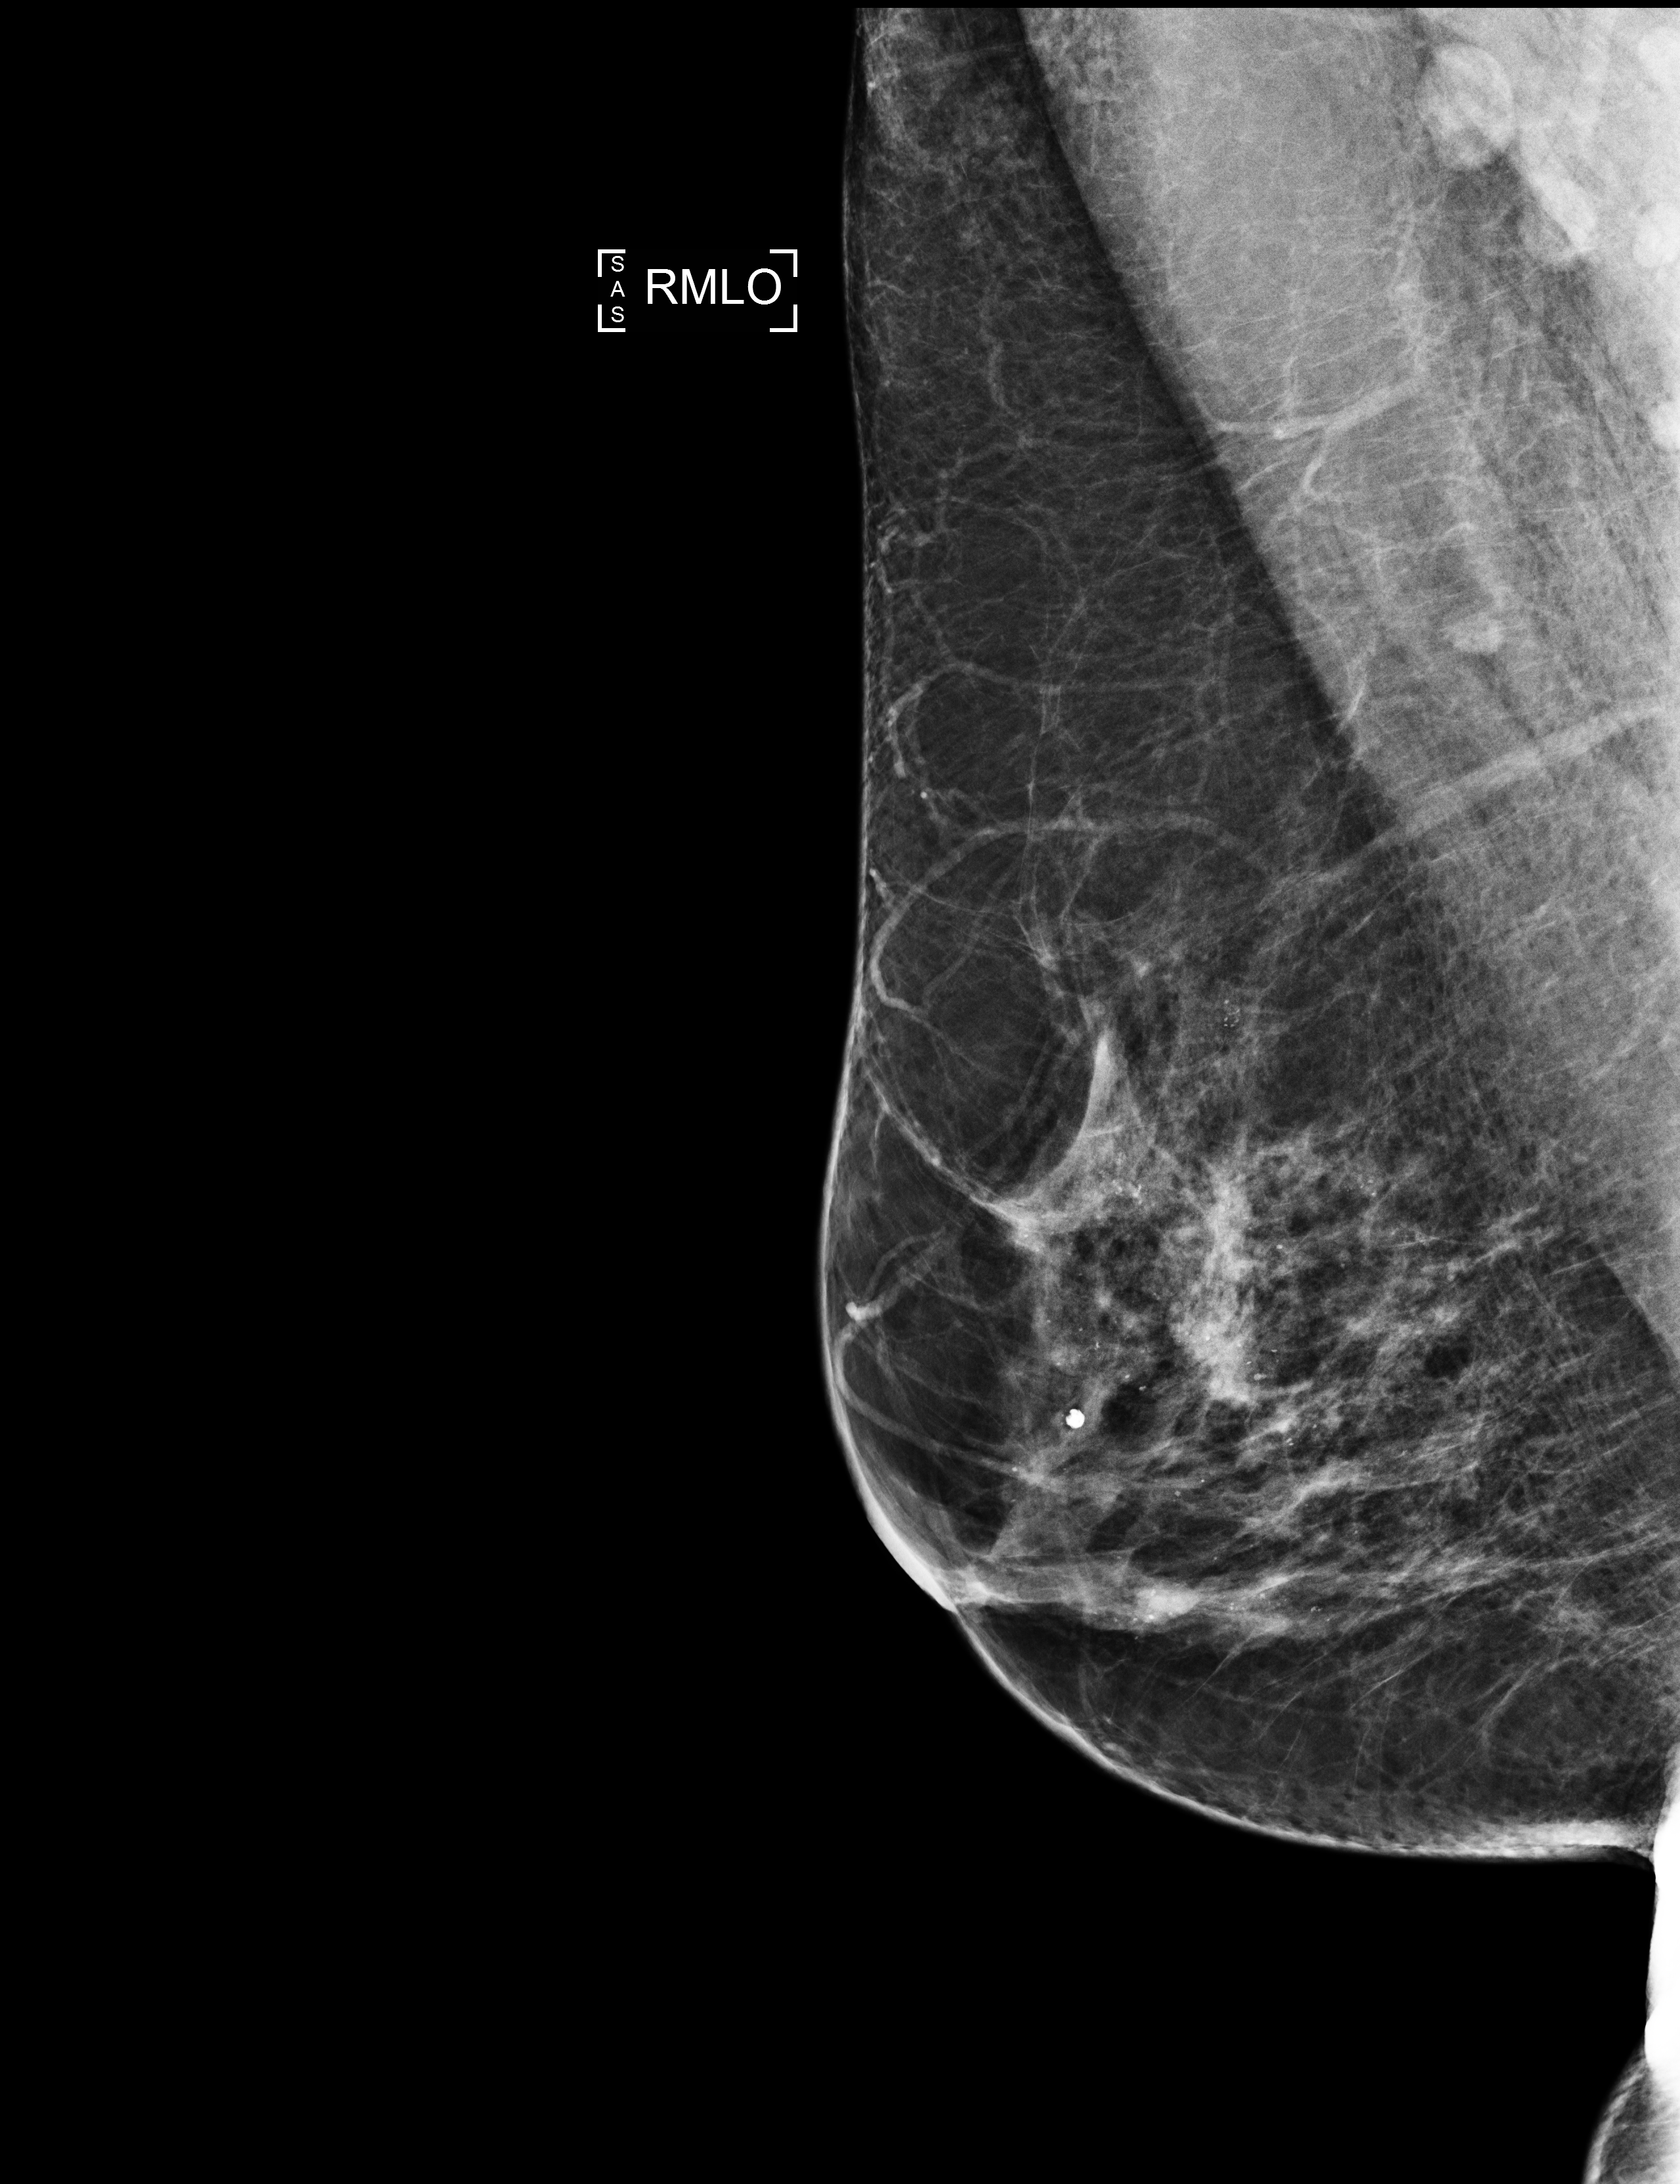
Annual screening mammography examination. Female patient, age 51 years.
Image type: full-field digital mammogram. Breast: right. Projection: mediolateral oblique (MLO) view.